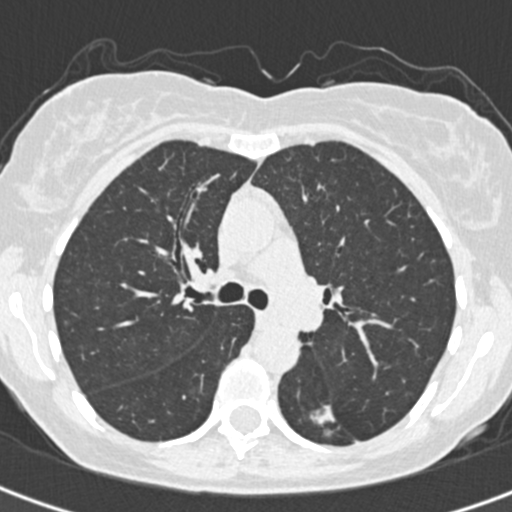
Low-dose screening chest CT, one axial slice. Lung window (W 1500 / L -600 HU). 1 mm slice thickness. 512 × 512 image matrix, field of view 284 × 284 mm.
Structures marked on this image (outlined manually by an expert reader):
- lesion 1 (tumor, lower lobe of left lung): bounding box <312,406,334,425> (left, top, right, bottom; pixels)